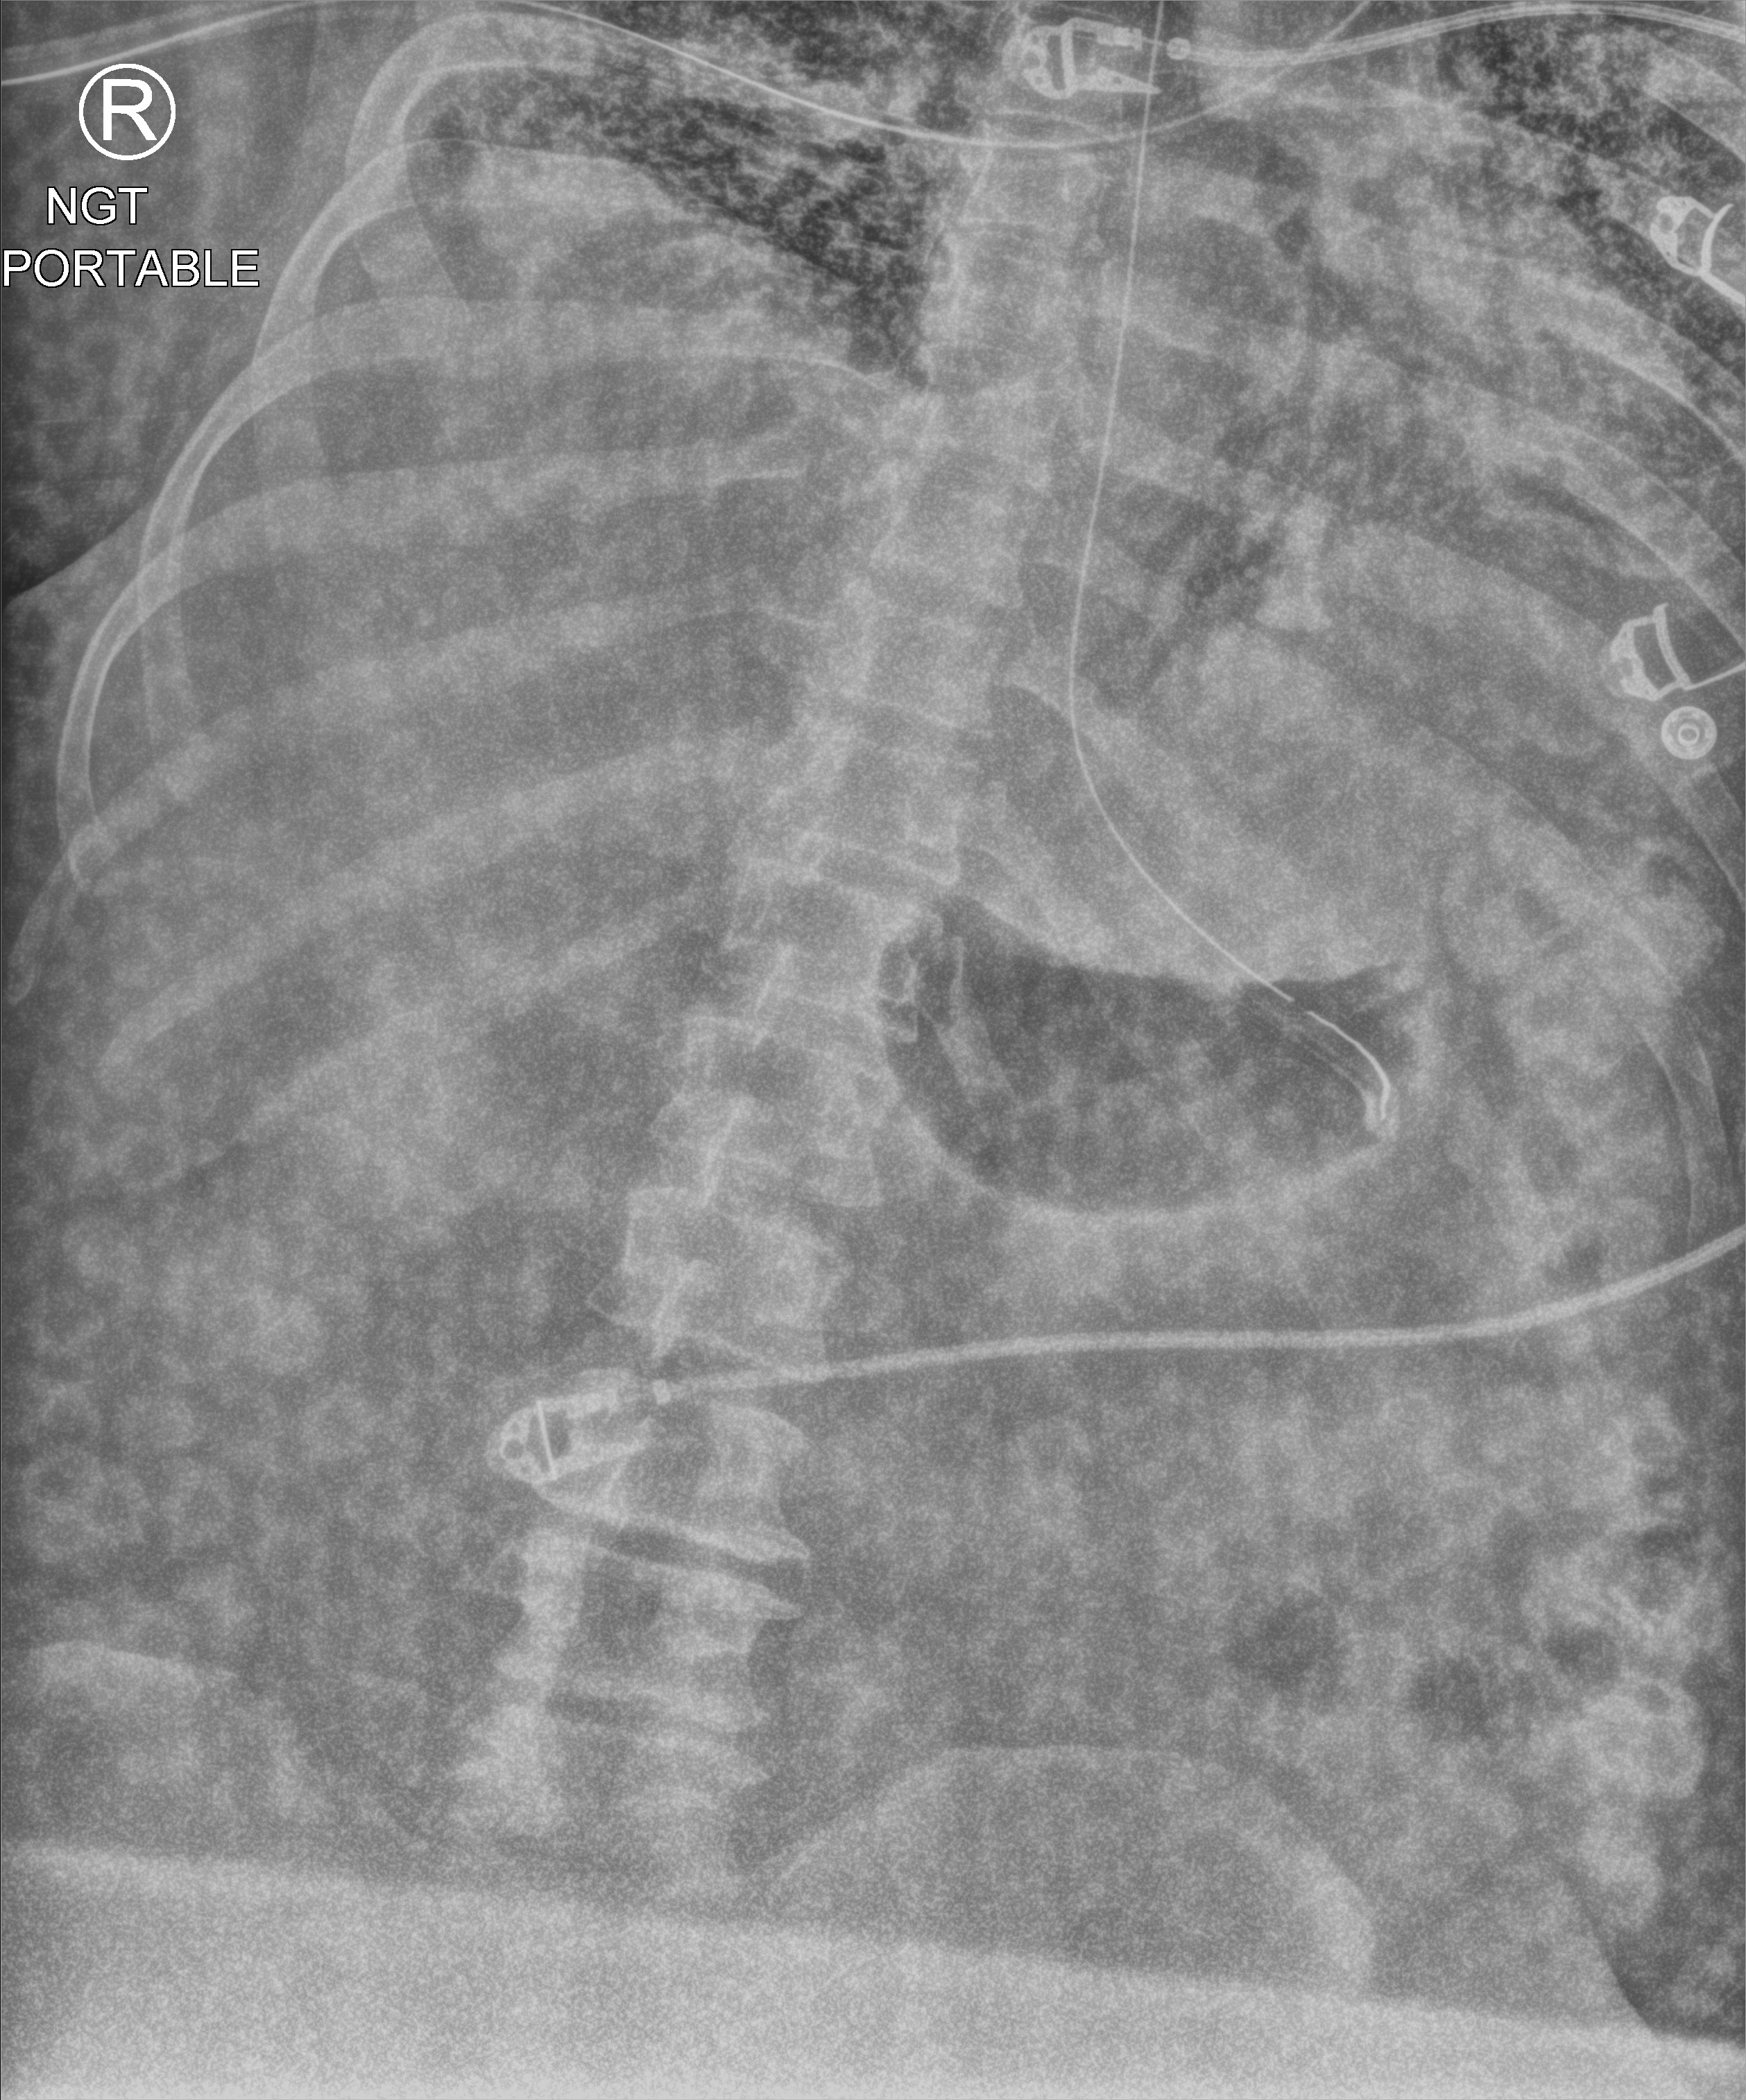
Abdomen X-ray (portable); anteroposterior (AP) projection. Male patient hospitalised with COVID-19, age 18–59 years.
From the hospital-stay record, not from the radiograph (when in the stay this image was taken is not recorded): mechanically ventilated during this hospital stay: yes; admitted to intensive care during this hospital stay: yes.